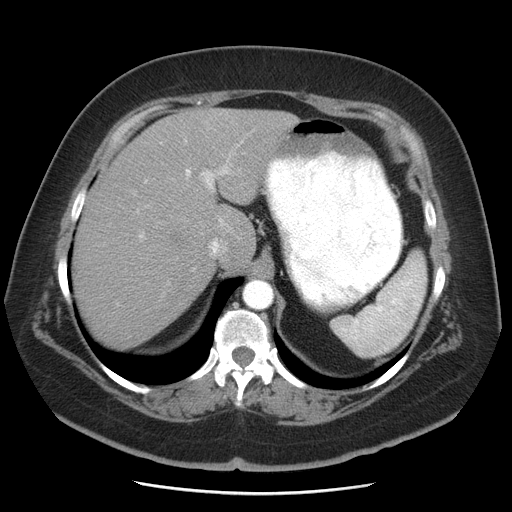
Contrast-enhanced abdominal CT, one axial slice; position 36 of 55 along the scan axis; reconstruction kernel STANDARD; 120 kVp; soft-tissue window (W 400 / L 40 HU); 5 mm slice thickness; 512 × 512 image matrix, field of view 380 × 380 mm. Female patient, age 52 years. Case-level facts recorded for this patient, not image findings: diagnosis: colorectal cancer liver metastases, imaged before liver resection; multiple liver metastases: yes; largest metastasis: 2.5 cm; disease in both lobes: yes.
Outlined on this slice (outlined manually by an expert reader):
- hepatic veins: bounding box (x1, y1, x2, y2) in pixels: (209, 239, 226, 256)
- liver: (72, 108, 299, 350)
- planned liver remnant (the part of the liver to remain after resection): (71, 165, 214, 350)
- portal vein (with intrahepatic branches): (138, 138, 243, 247)
- liver metastasis: (217, 118, 238, 133)